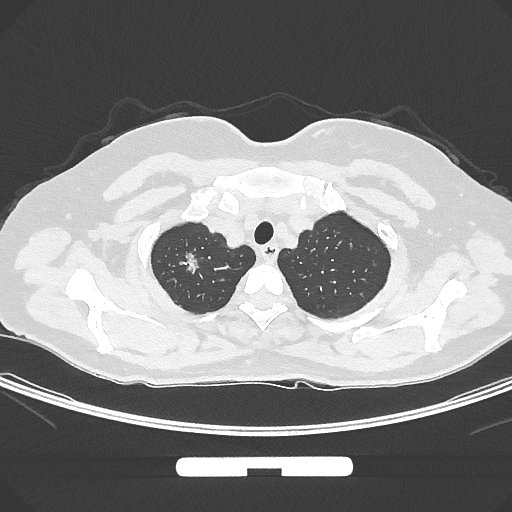
Chest CT, one axial slice; position 259 of 294 along the scan axis; lung window (W 1500 / L -600 HU); 512 × 512 image matrix. Patient: female, 58 years. Case-level facts recorded for this patient, not image findings: clinical TNM (as recorded): T1b N0 M0.
Structures marked on this image (bounding box drawn by a radiologist):
- lung tumour (recorded histology: adenocarcinoma): bounding box (x1, y1, x2, y2) in pixels: (178, 246, 205, 283)